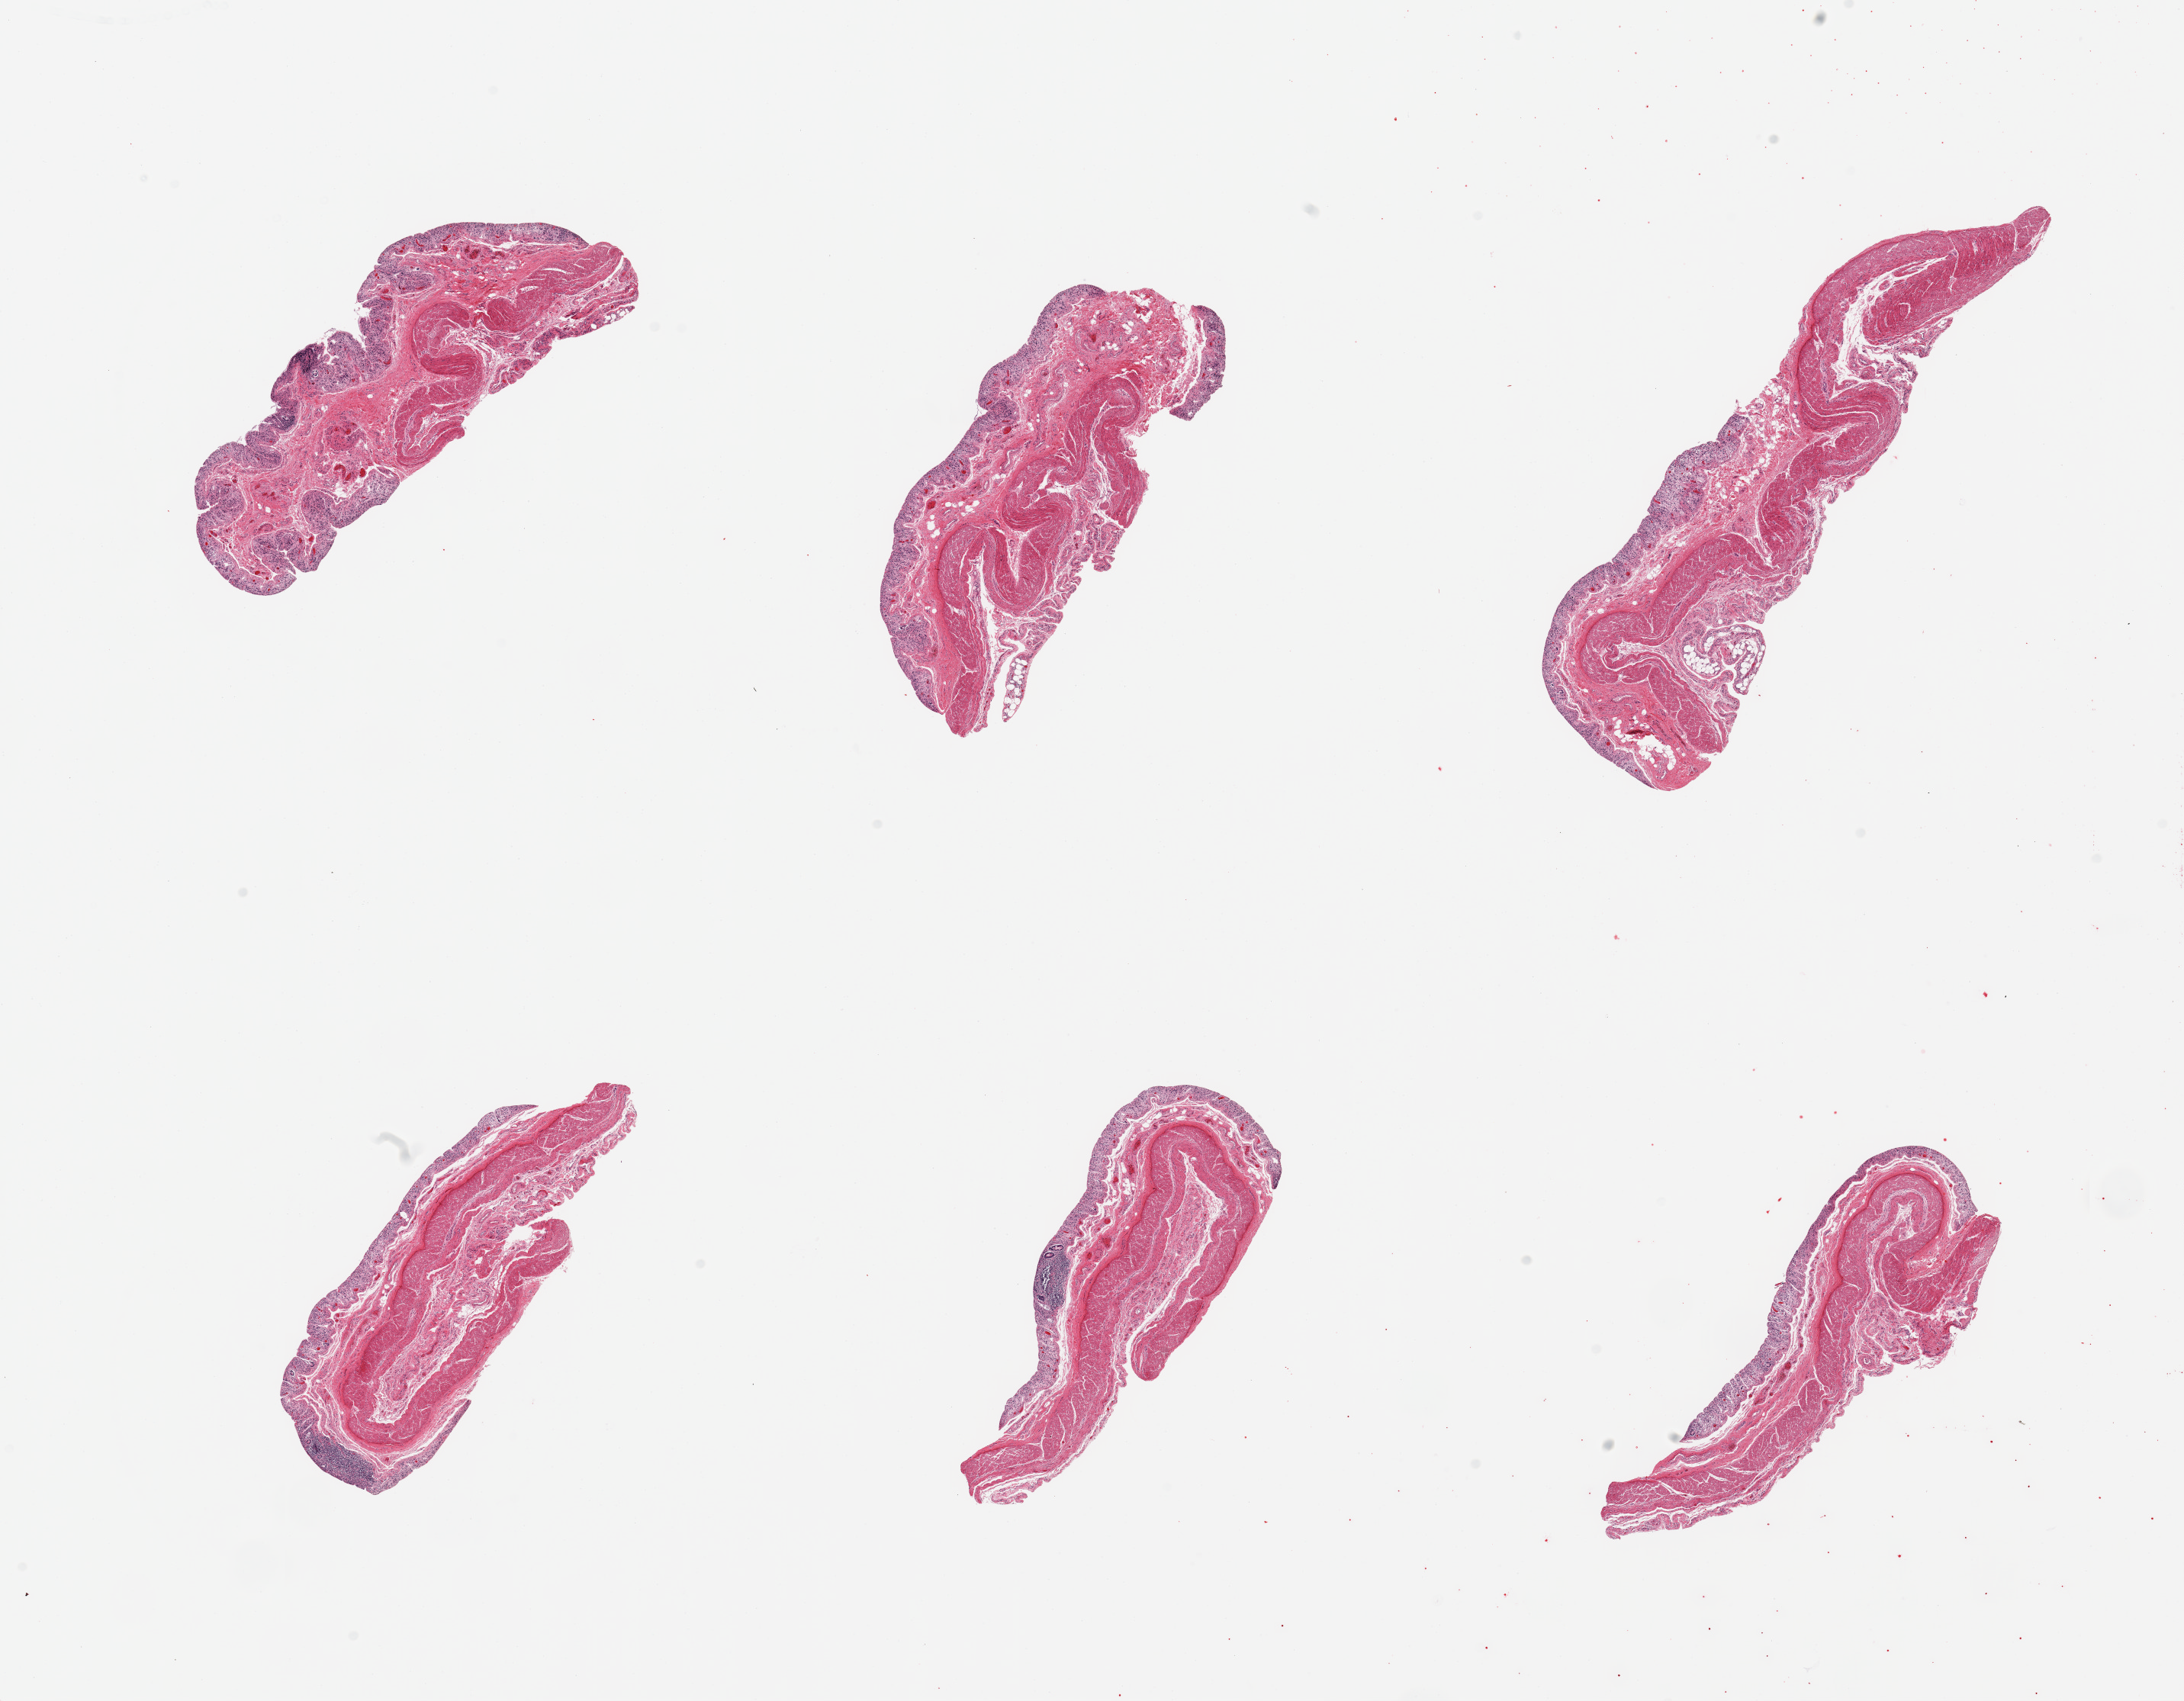
Digitized hematoxylin and eosin (H&E)-stained section, brightfield, low-resolution overview of the scanned area, about 22.6 x 17.6 mm. PAXgene-fixed, paraffin-embedded tissue. Target tissue: transverse colon. Donor tissue sample. Donor sex: male.
• review note (as recorded): 6 pieces, mucosa ~0.2mm, completely autolyzed